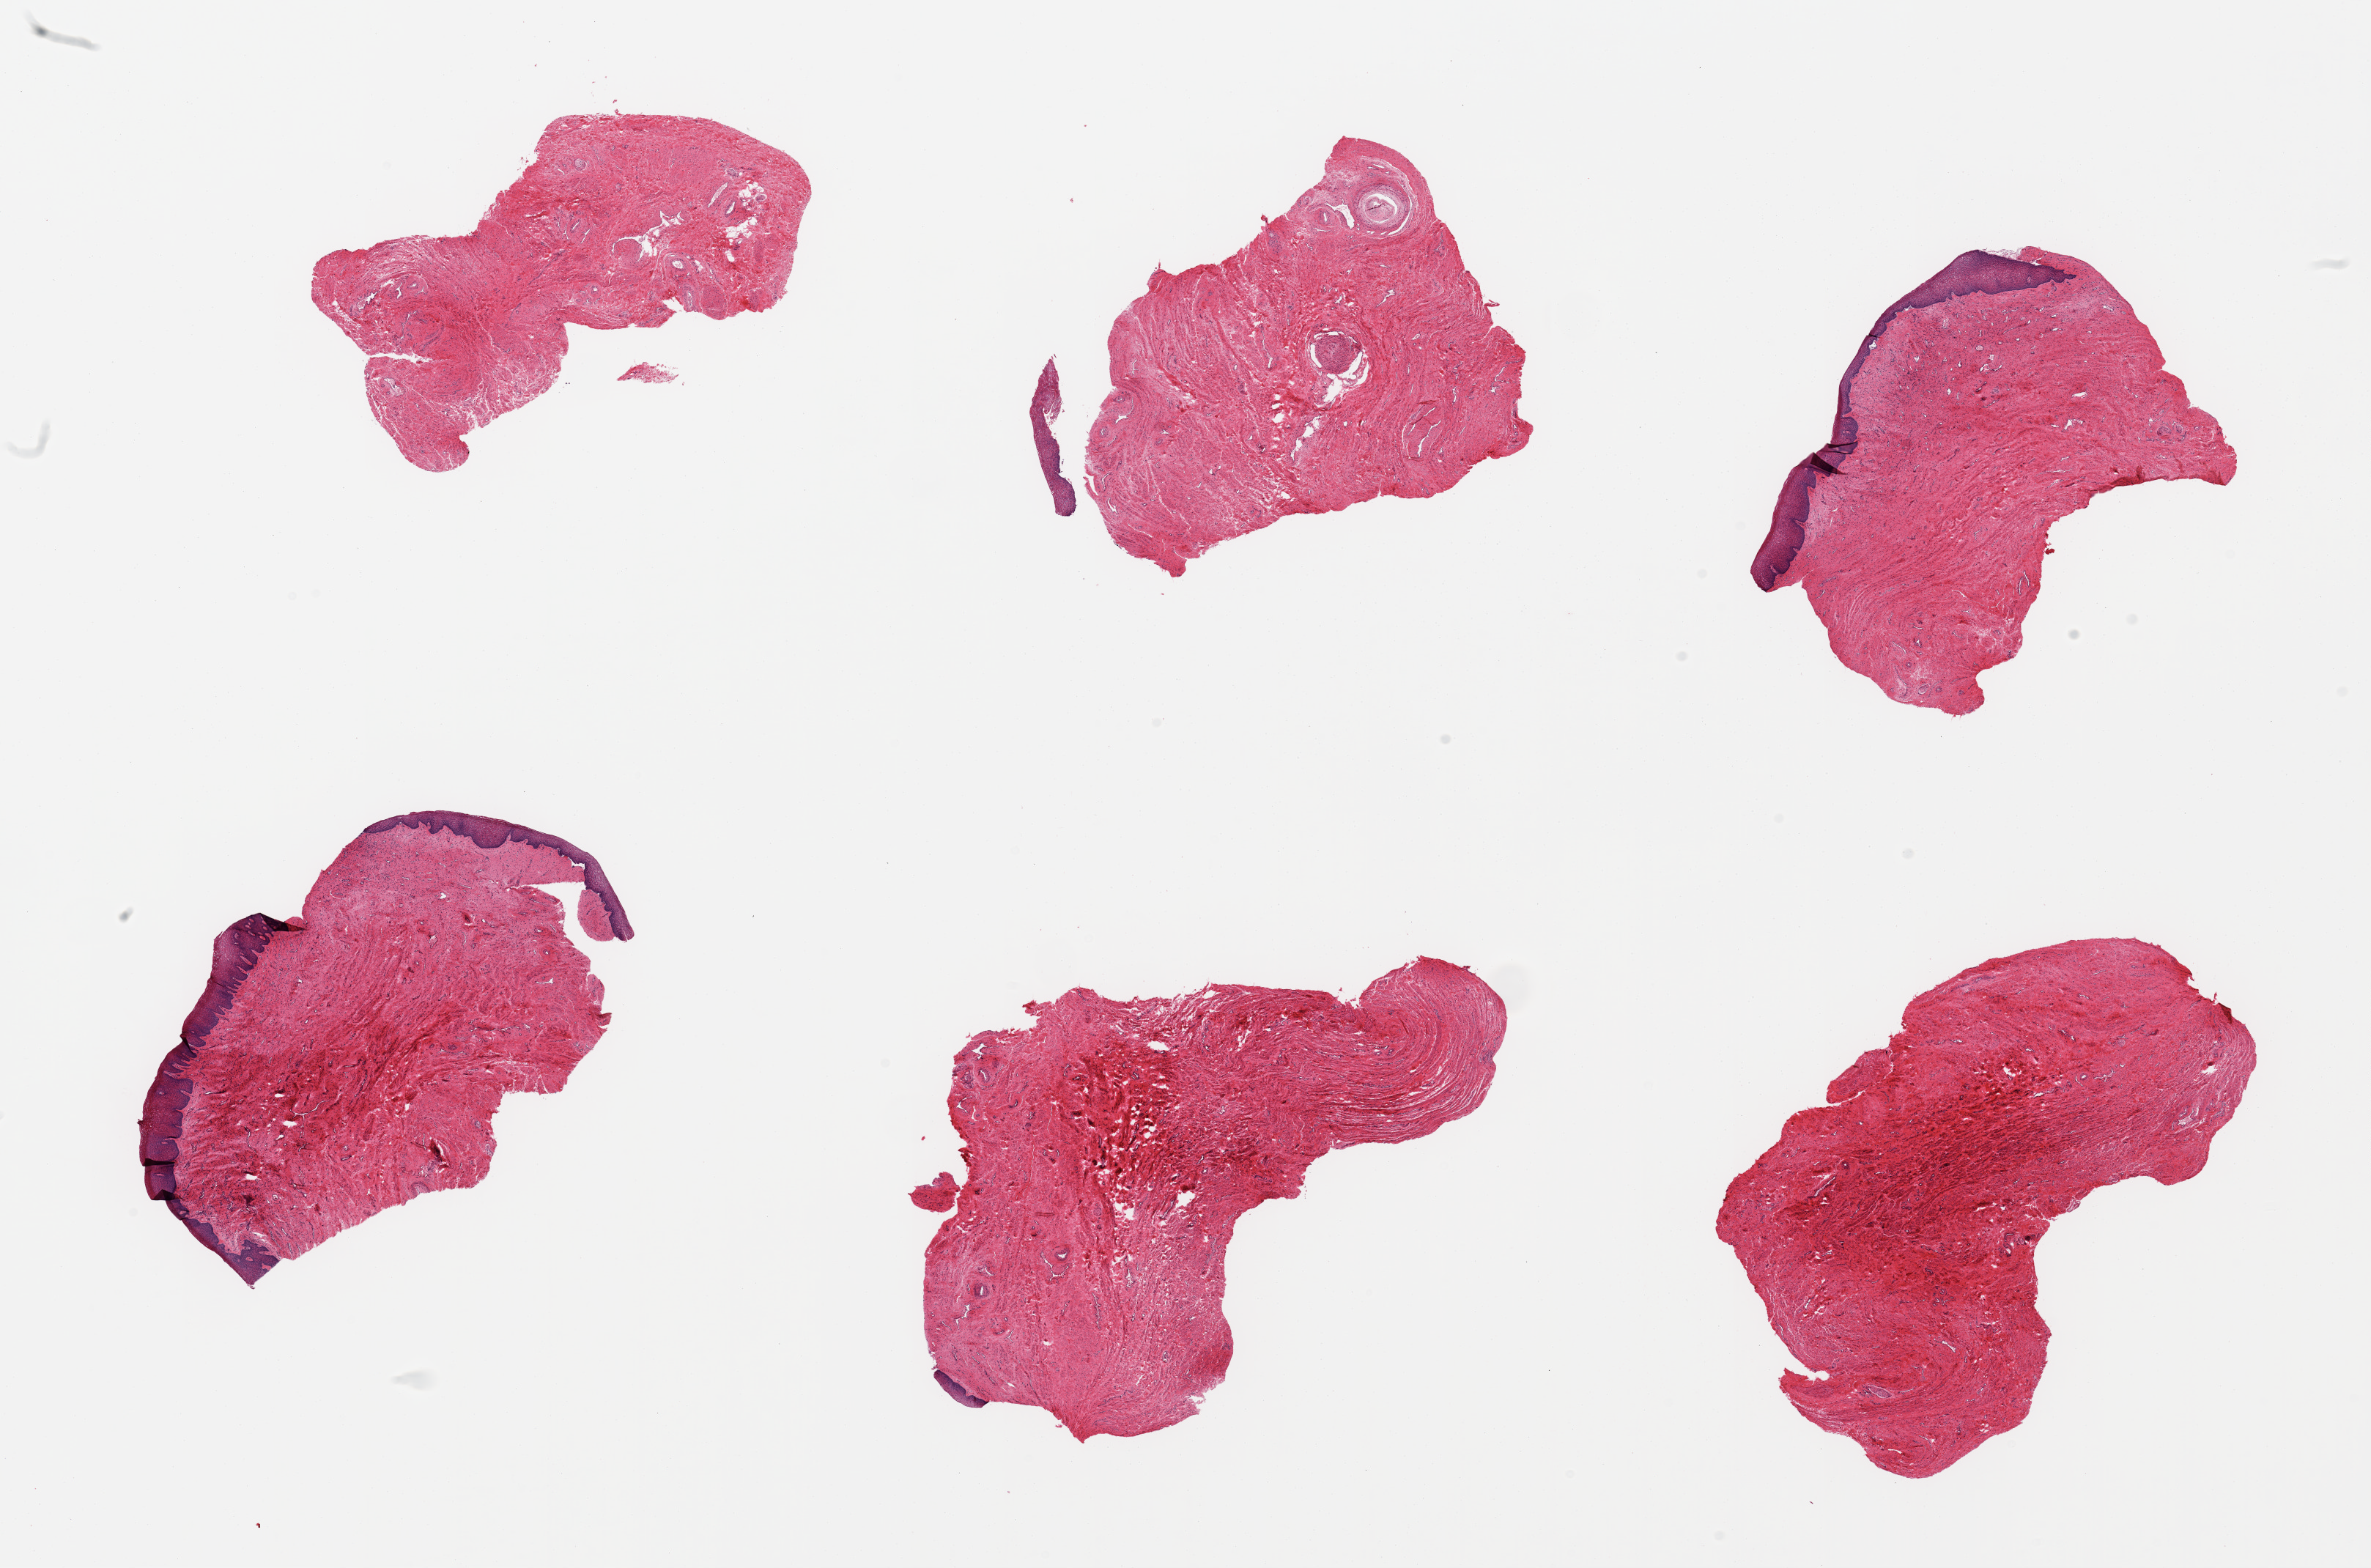
Hematoxylin and eosin (H&E) whole-slide image, low-resolution overview of the scanned area, about 25.6 x 16.9 mm, PAXgene-fixed, paraffin-embedded tissue, sampled site (target tissue): vagina, tissue donor sample. Donor sex: female.
• review note (as recorded): 6 pieces; 3 of 6 pieces contain squamous epithelium